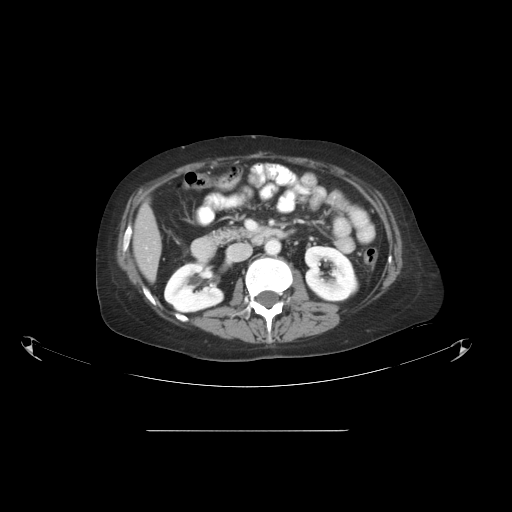
Contrast-enhanced abdominal CT, one axial slice. Slice 22 of 51 in the series (ordered by position). Intravenous contrast given. Soft-tissue window (W 400 / L 40 HU). 512 × 512 image matrix, field of view 475 × 475 mm. Female patient, age 48 years. From the clinical record (not read from this slice): diagnosis: colorectal cancer liver metastases, imaged before liver resection; multiple liver metastases: yes; largest metastasis: 1 cm; chemotherapy before resection: no.
Outlined on this slice (outlined manually by an expert reader):
- liver: box from (x=135, y=206) to (x=161, y=280) px
- planned liver remnant (the part of the liver to remain after resection): (x=135, y=206)–(x=161, y=280)